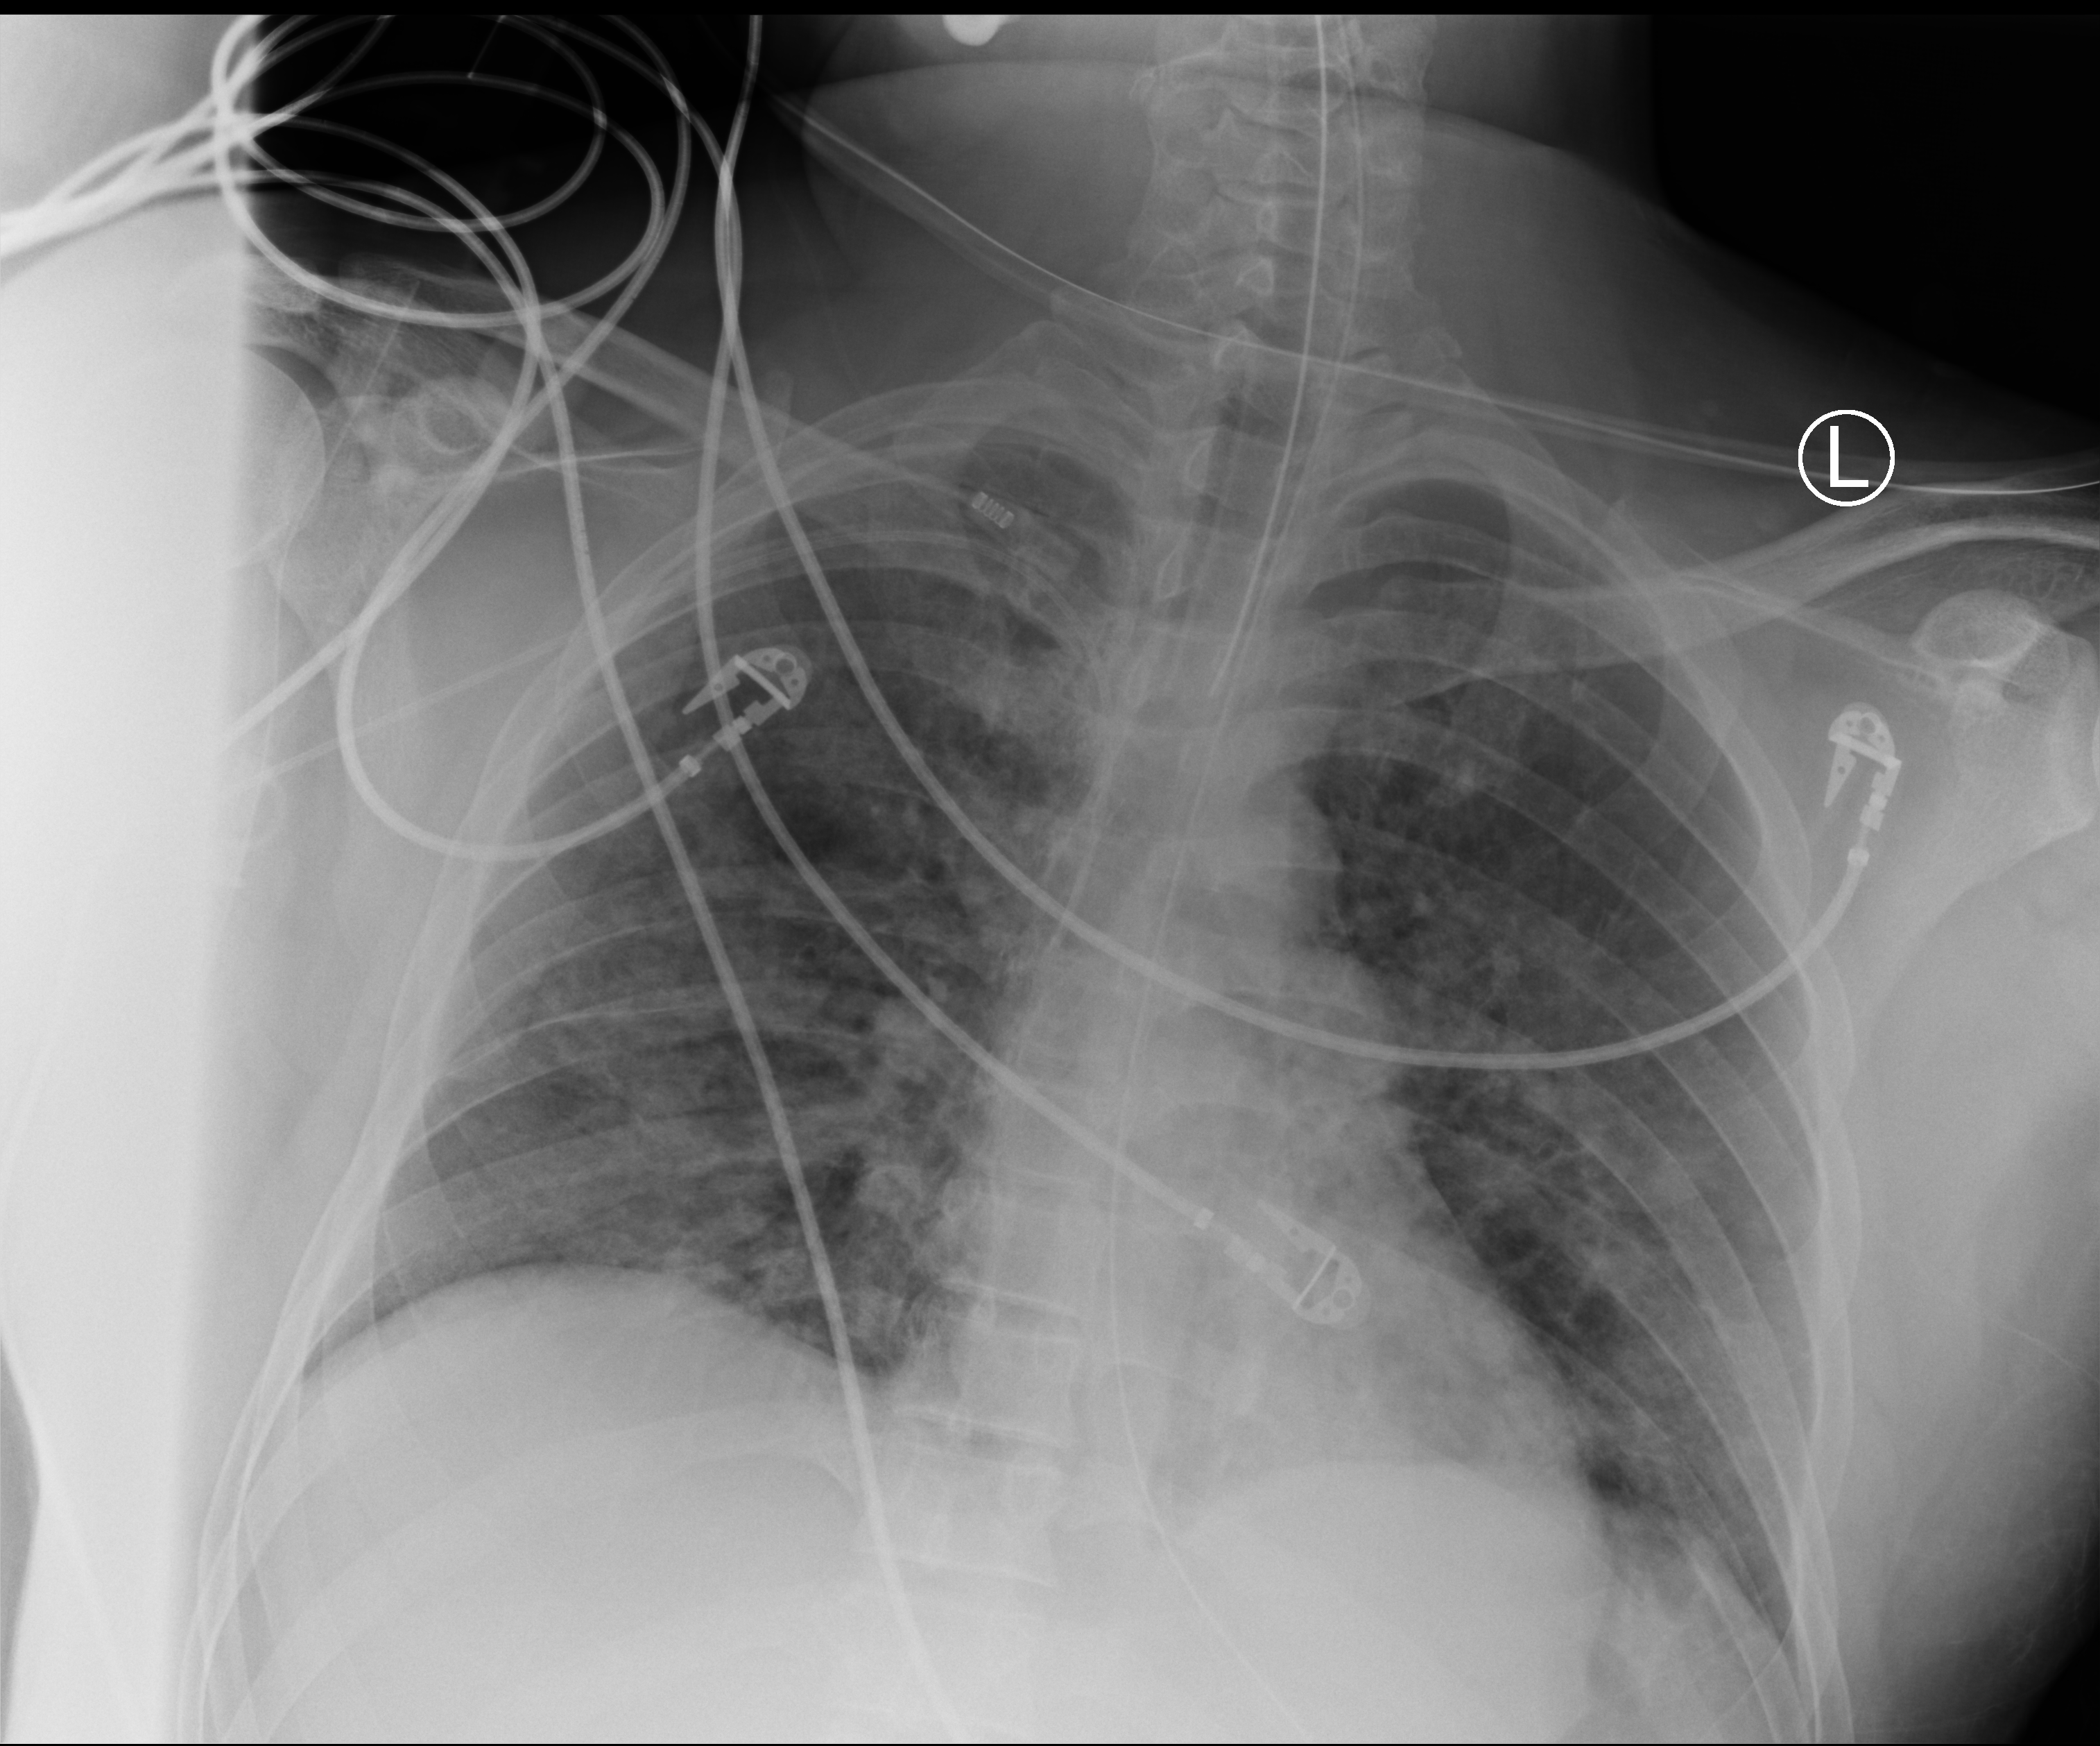
Bedside chest radiograph (computed radiography), anteroposterior (AP) projection. Patient hospitalised with COVID-19, aged 18–59 years.
Hospital-stay facts (about this admission, not read from this image; timing relative to this image not recorded): mechanically ventilated during this hospital stay: yes; admitted to intensive care during this hospital stay: yes.